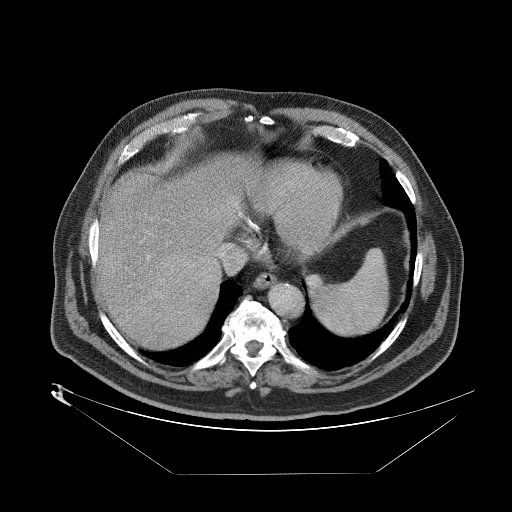
Contrast-enhanced abdominal CT (liver protocol), one axial slice; slice 71 of 89 in the series (ordered by position); 140 kVp; one of 2 acquisitions stored at this slice position; soft-tissue window (W 400 / L 40 HU); 512 × 512 image matrix, field of view 480 × 480 mm. From the clinical record (not read from this slice): diagnosis: hepatocellular carcinoma (patient treated with transarterial chemoembolisation; whether this scan precedes or follows treatment is not stated here); TNM stage (as recorded): Stage-II; Child-Pugh class: B; tumour size: 4 cm.
Outlined on this slice (semi-automatically segmented with operator editing):
- abdominal aorta: box from (x=268, y=284) to (x=303, y=318) px
- liver parenchyma outside the tumour (the mass and vessels are separate outlines, so this box may not span the whole liver): (x=92, y=160)–(x=254, y=342)
- mass: (x=151, y=252)–(x=220, y=322)
- liver vessels: (x=95, y=196)–(x=239, y=310)